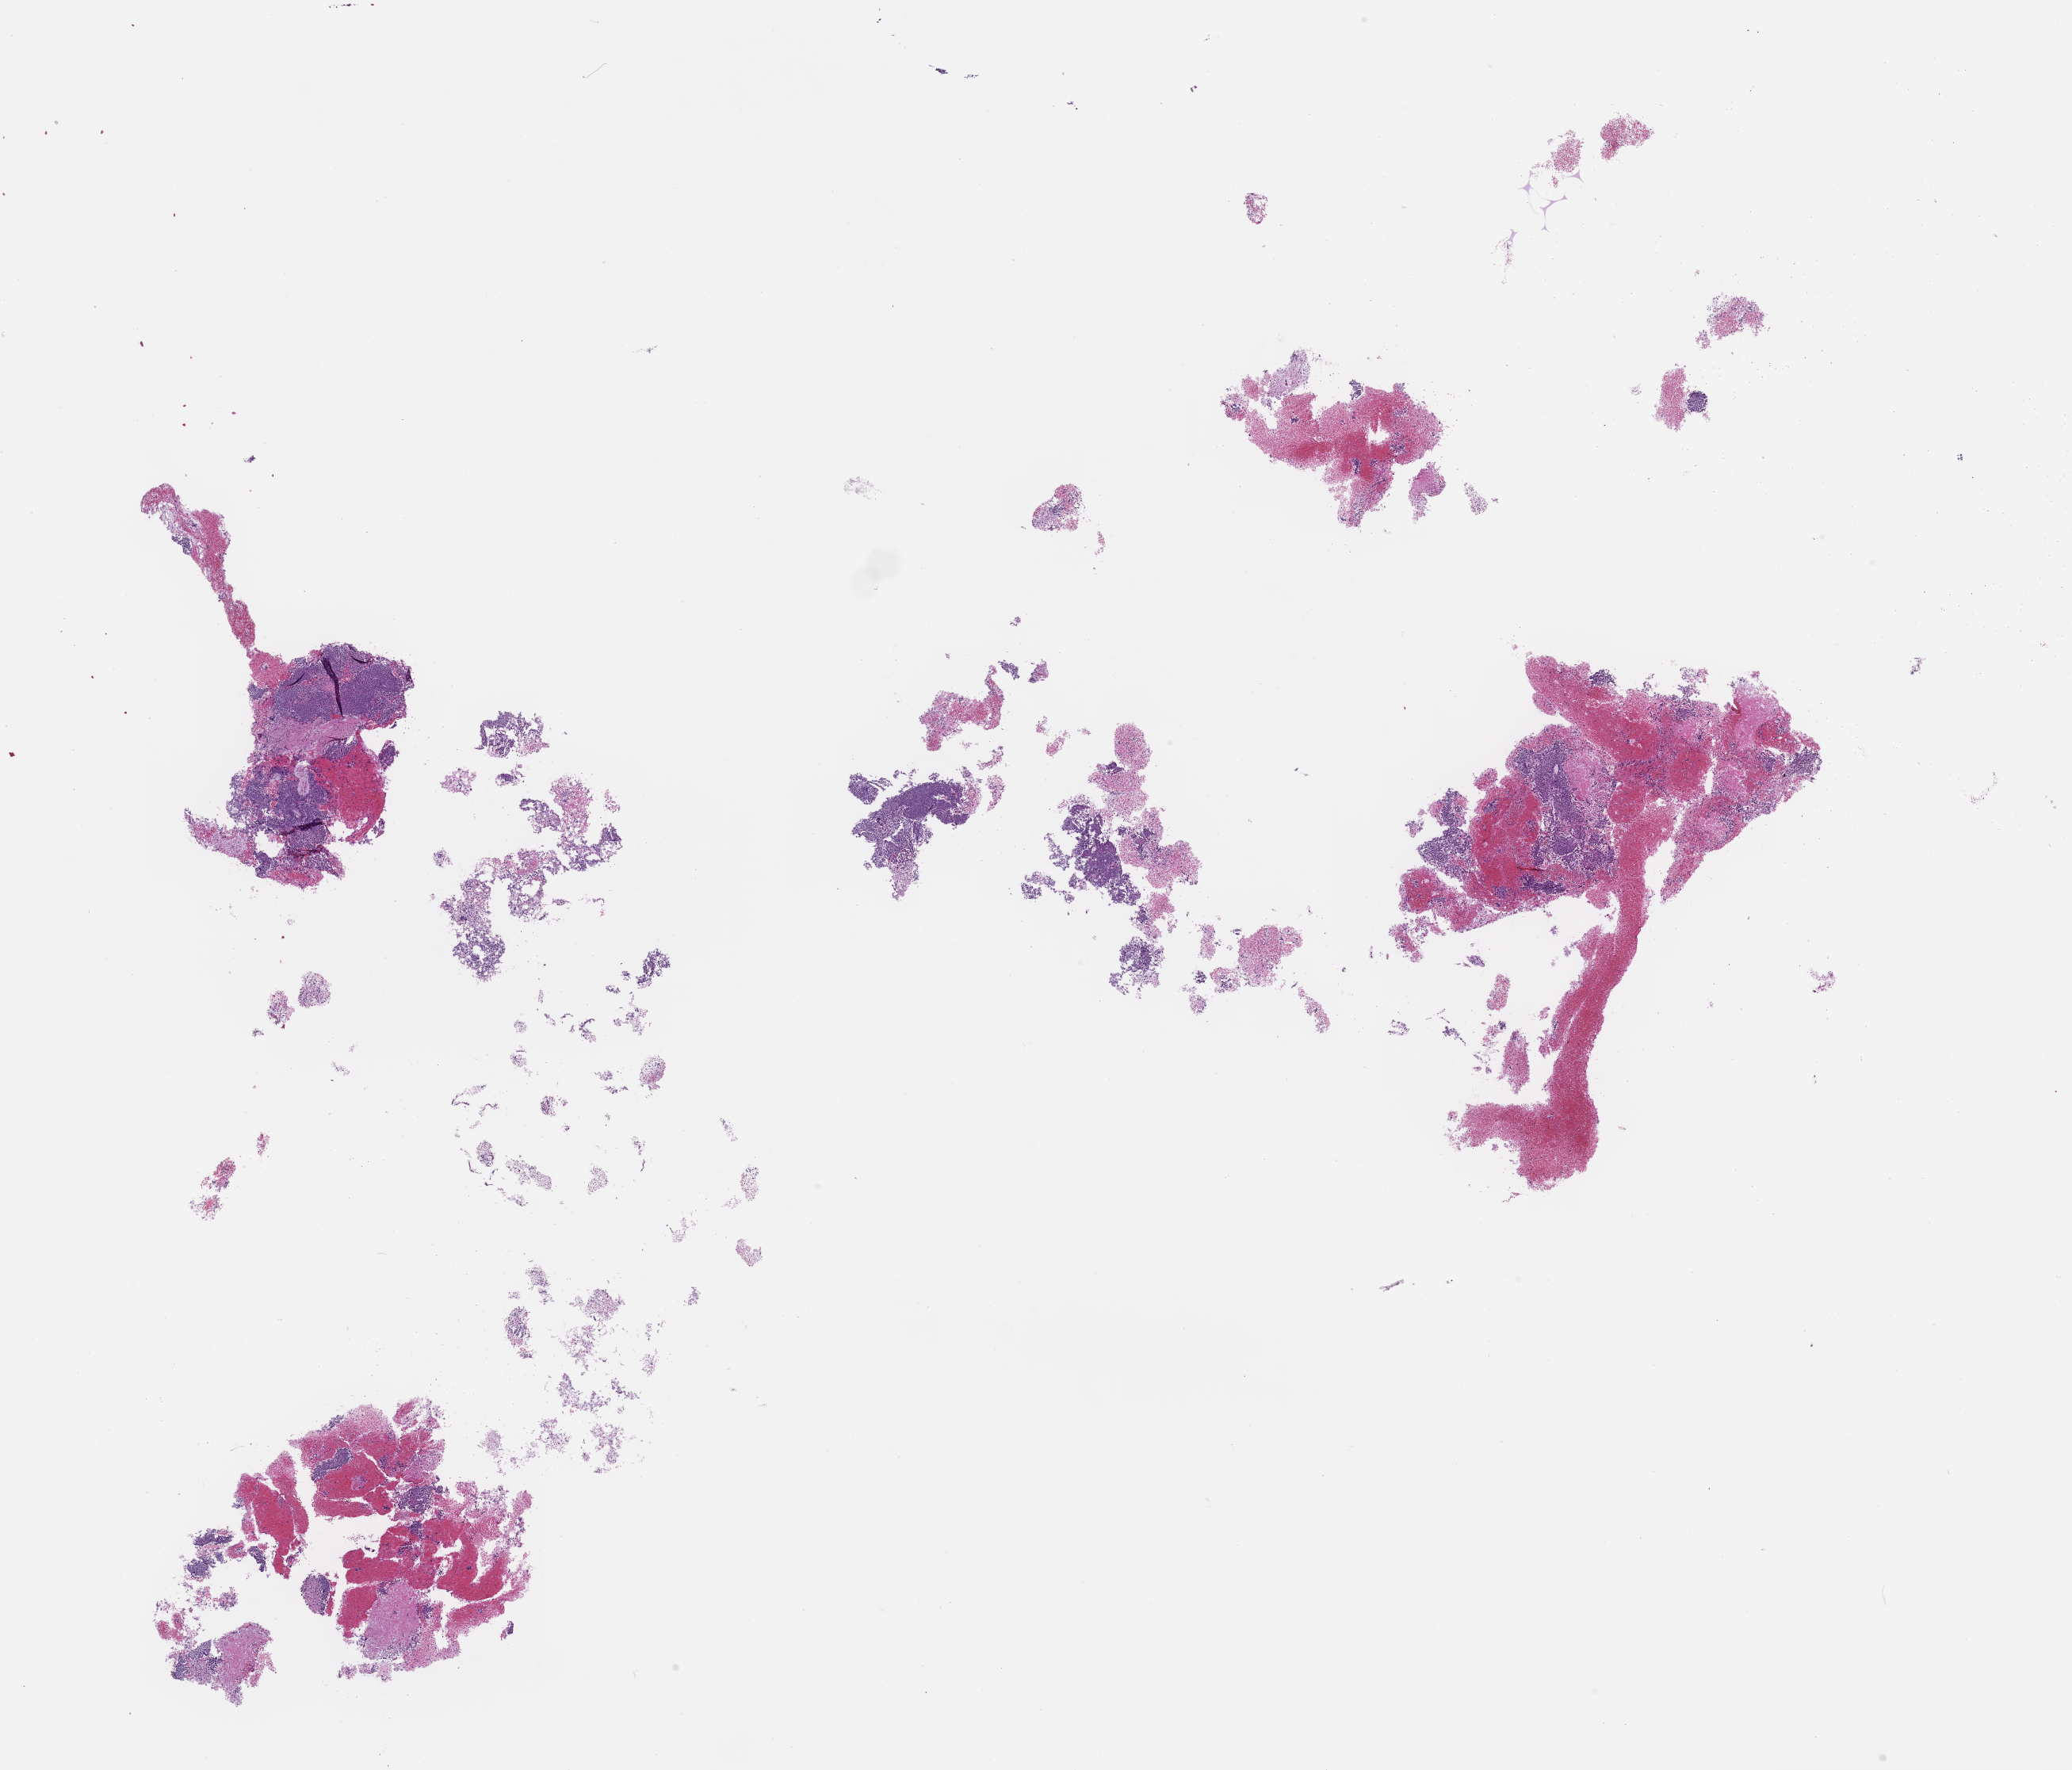
Whole-slide image, hematoxylin and eosin (H&E) stain, low-resolution overview of the scanned area, about 21.1 x 18.0 mm. FFPE section. Collected at disease progression. Patient sex: male.
This section: metastatic tumor tissue. Primary diagnosis of the patient: Prostate Carcinoma.